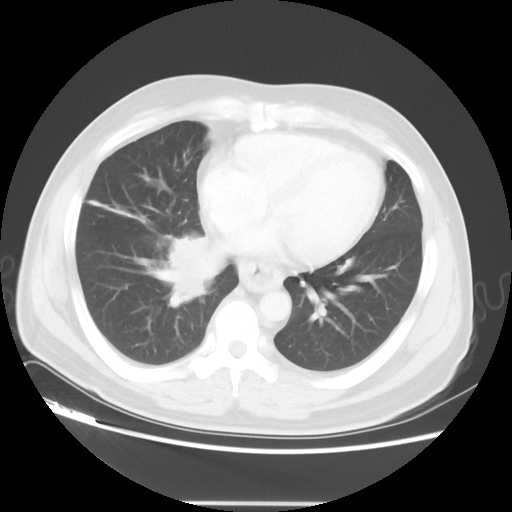
Chest CT, one axial slice; slice 19 of 48 in the series (ordered by position); 120 kVp; lung window (W 1500 / L -600 HU); 5 mm slice thickness; 512 × 512 image matrix, field of view 390 × 390 mm. Male patient, age 53 years. From the clinical record (not read from this slice): clinical TNM (as recorded): T2 N3 M0; histopathological grade: G3.
Structures marked on this image (rectangle marked by the reading radiologist):
- lung tumour (recorded histology: small cell carcinoma): bounding box [x1, y1, x2, y2] px = [154, 225, 215, 306]